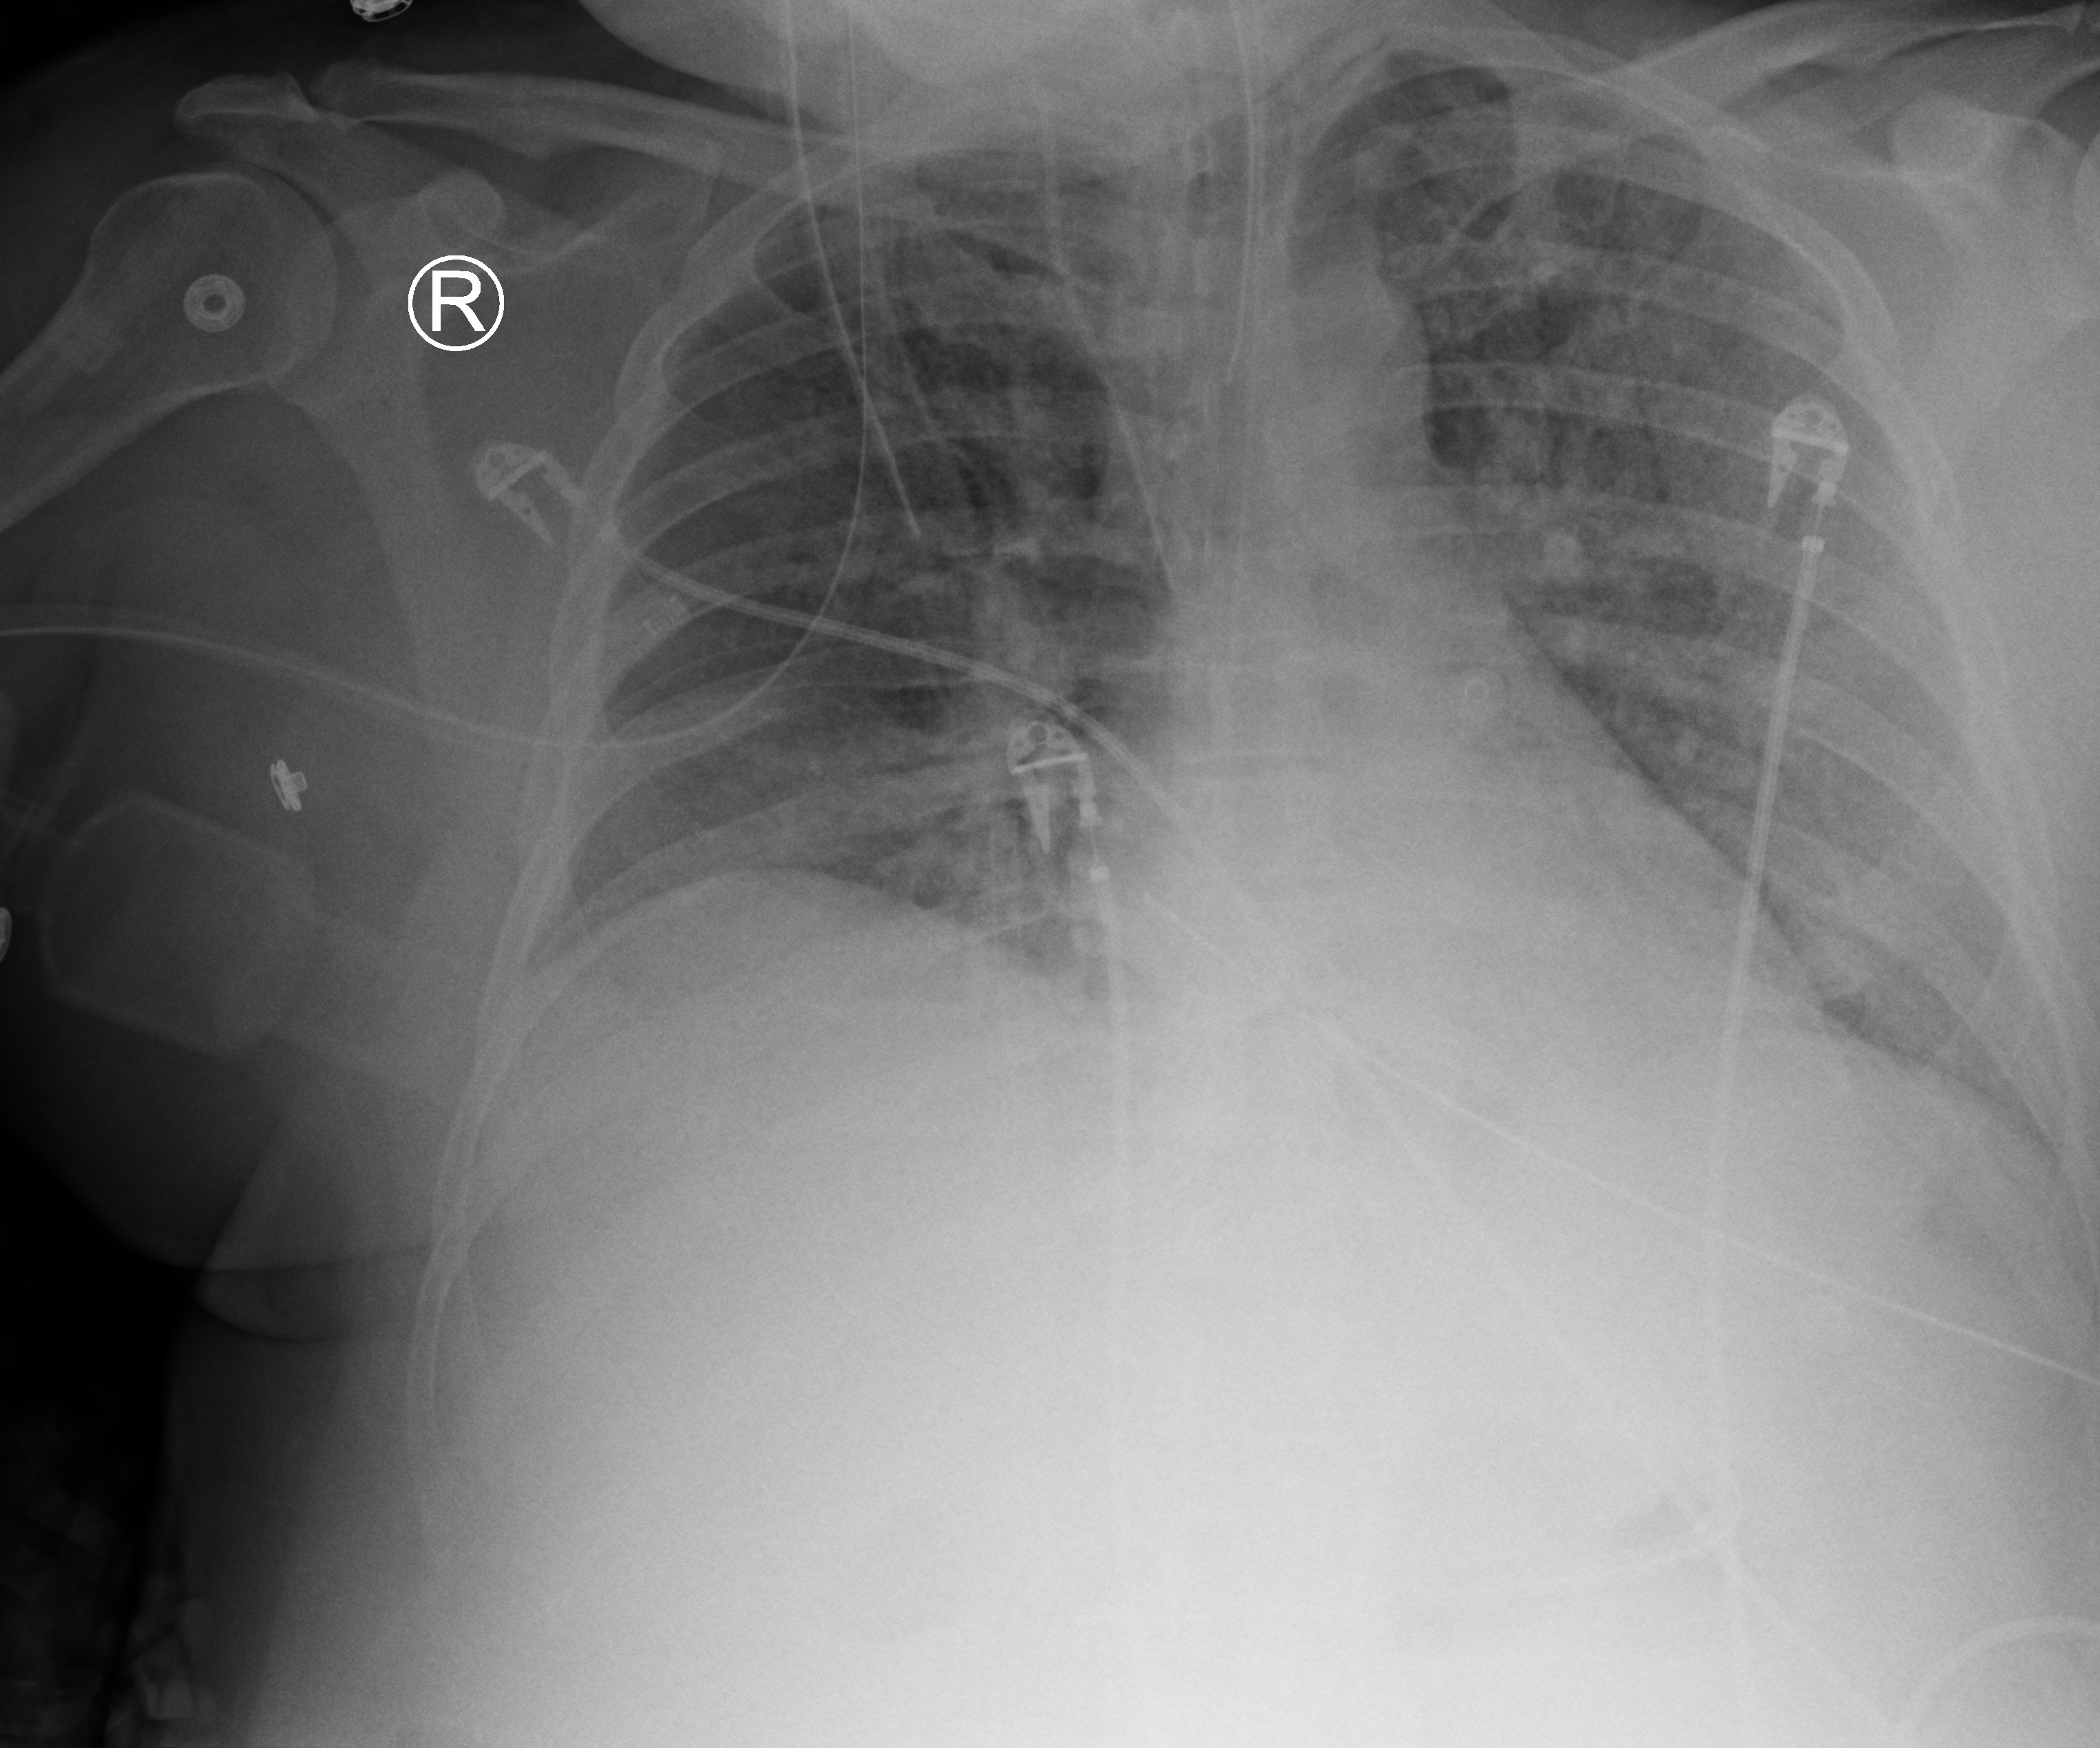
Bedside chest radiograph (computed radiography). Patient hospitalised with COVID-19; male, aged 18–59 years.
From the hospital-stay record, not from the radiograph (when in the stay this image was taken is not recorded):
- admitted to intensive care during this hospital stay: yes
- mechanically ventilated during this hospital stay: yes